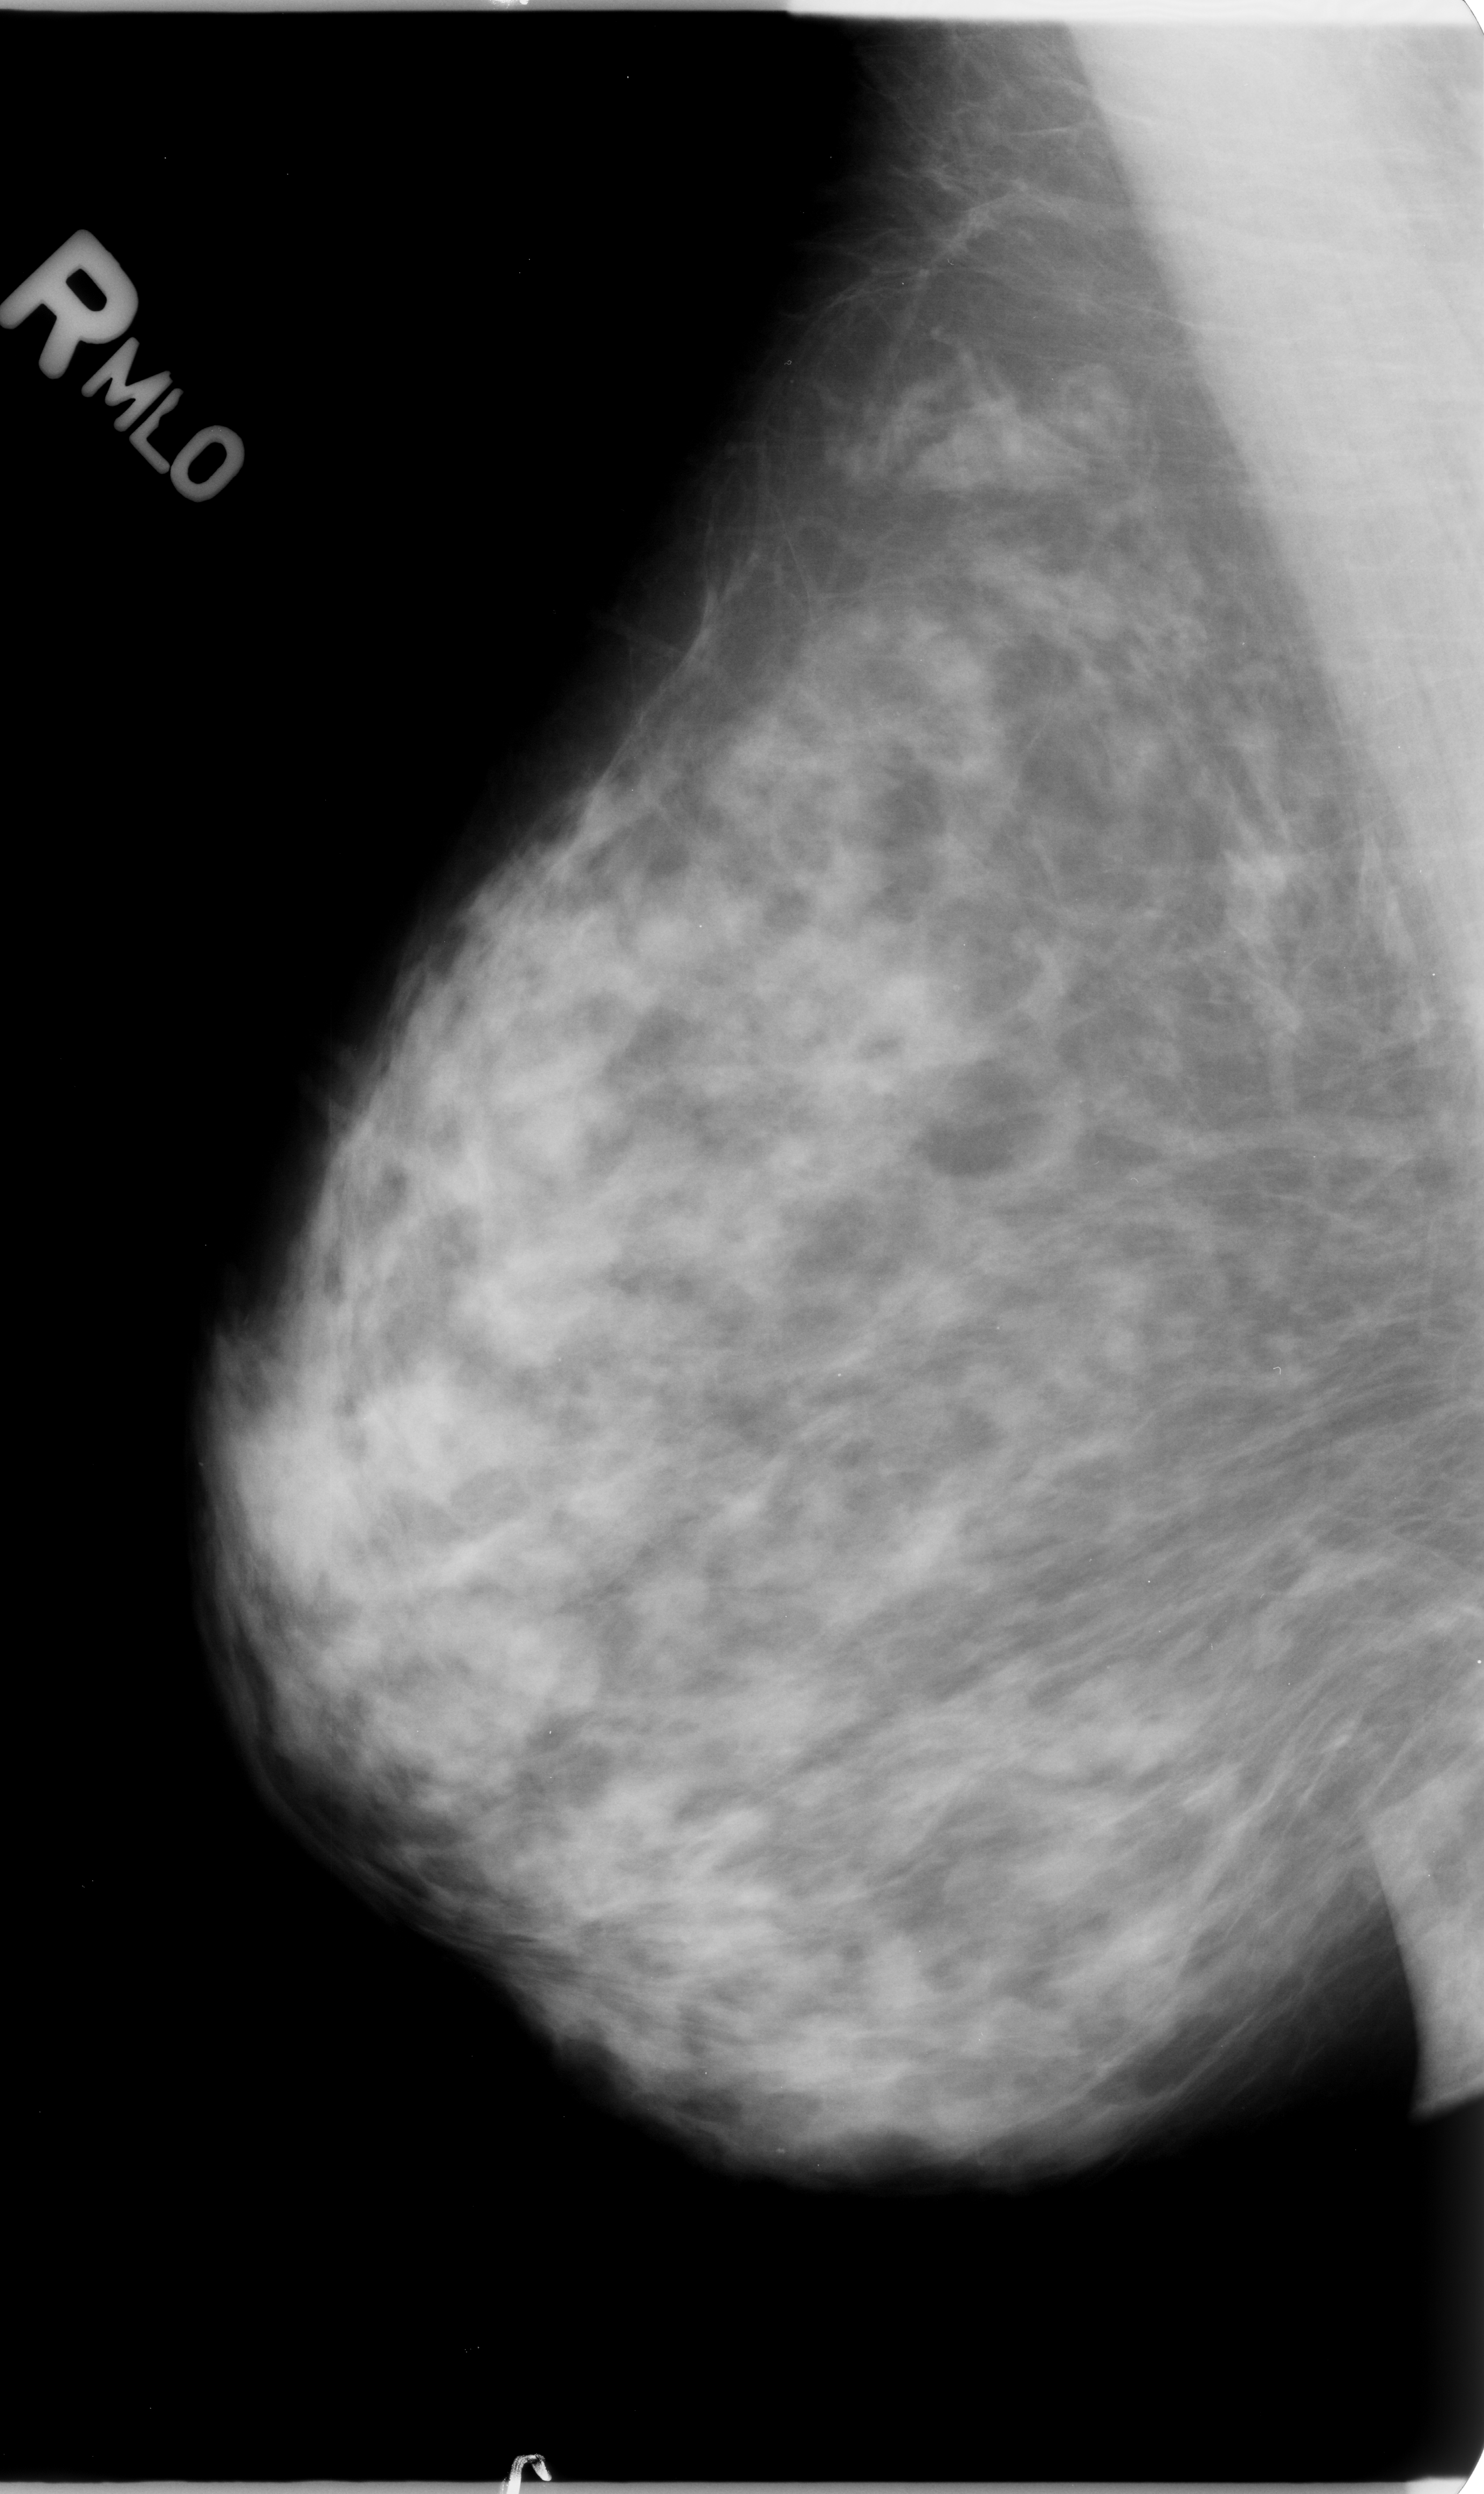
Digitized screen-film mammogram. Right breast. Mediolateral oblique (MLO) view. BI-RADS breast density category 3 (scale 1–4). 1484 × 2494 image matrix.
Expert-marked regions of interest on this film, with their recorded descriptors:
- calcifications, morphology pleomorphic, distribution clustered; BI-RADS assessment category 4; pathology (as recorded): benign: bounding box (x1, y1, x2, y2) in pixels: (767, 599, 1015, 791)